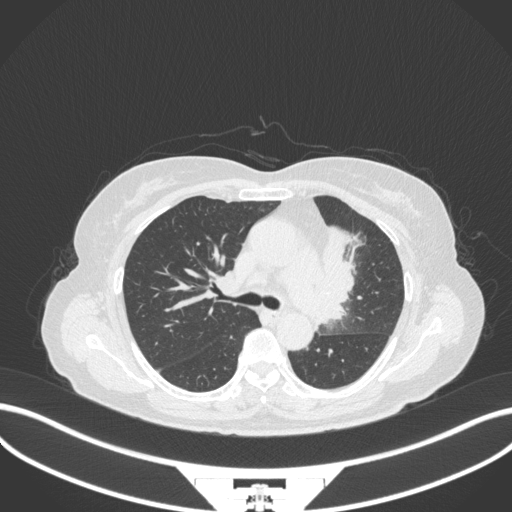
Chest CT, one axial slice. Slice 216 of 382 in the series (ordered by position). Reconstruction kernel B31f. Lung window (W 1500 / L -600 HU). 1 mm slice thickness. 512 × 512 image matrix. Patient: female, 64 years. Case-level facts recorded for this patient, not image findings: clinical TNM (as recorded): T2a N2 M0.
Outlined on this slice (rectangle marked by the reading radiologist):
- lung tumour (recorded histology: adenocarcinoma): box from (x=324, y=220) to (x=363, y=321) px